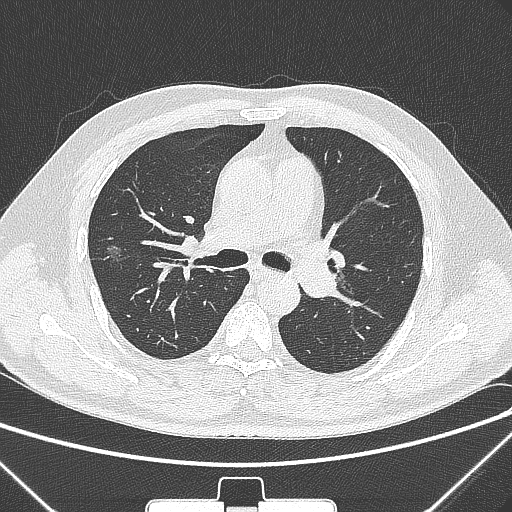
Chest CT, one axial slice. Position 192 of 320 along the scan axis. Lung window (W 1500 / L -600 HU). 512 × 512 image matrix, field of view 350 × 350 mm. Patient: male, 58 years. Case-level facts recorded for this patient, not image findings: clinical TNM (as recorded): T1c N0 M0.
Outlined on this slice (bounding box drawn by a radiologist):
- lung tumour (recorded histology: adenocarcinoma): bounding box [x1, y1, x2, y2] px = [100, 239, 133, 269]